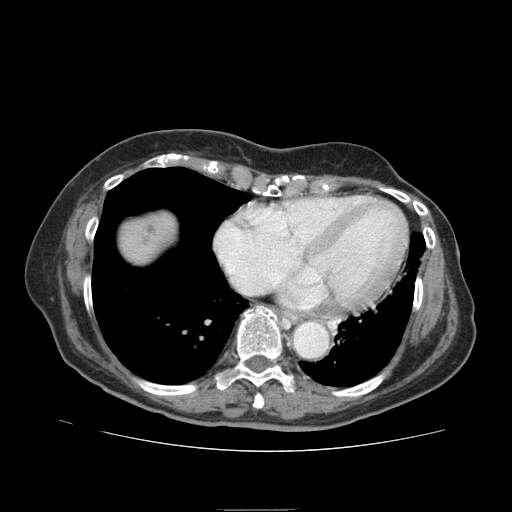
Contrast-enhanced abdominal CT (liver protocol), one axial slice. Slice 81 of 95 in the series (ordered by position). Reconstruction kernel STANDARD. 140 kVp. Soft-tissue window (W 400 / L 40 HU). 512 × 512 image matrix, field of view 360 × 360 mm. From the clinical record (not read from this slice): diagnosis: hepatocellular carcinoma (patient treated with transarterial chemoembolisation; whether this scan precedes or follows treatment is not stated here); TNM stage (as recorded): Stage-IVA; Child-Pugh class: B.
Outlined on this slice (semi-automatically segmented with operator editing):
- abdominal aorta: bounding box [x1, y1, x2, y2] px = [295, 322, 327, 357]
- liver parenchyma outside the tumour (the mass and vessels are separate outlines, so this box may not span the whole liver): [120, 212, 176, 262]